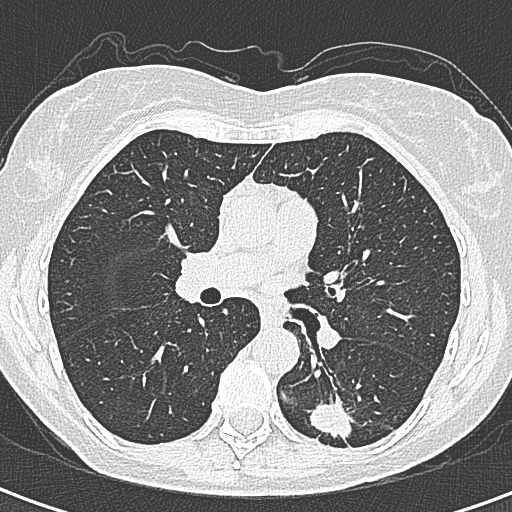
Axial slice from a low-dose chest CT screening exam. First (baseline) screen. Lung window (W 1500 / L -600 HU). 1 mm slice thickness. Lung (sharp) reconstruction kernel (B80f). 512 × 512 image matrix, field of view 284 × 284 mm. Female, age 58 years at enrolment. Former smoker at enrolment.
Lesion marked by an expert reader, bounding box <297,387,366,456> (left, top, right, bottom; pixels). The screening reader recorded 2 non-calcified nodules or masses ≥4 mm on this exam; which of them this box marks is not recorded. Participant outcome: lung cancer diagnosed 22 days after this screen — adenocarcinoma, NOS, left lower lobe, moderately differentiated (G2), stage IA (AJCC 6th edition), 25 mm at pathology.